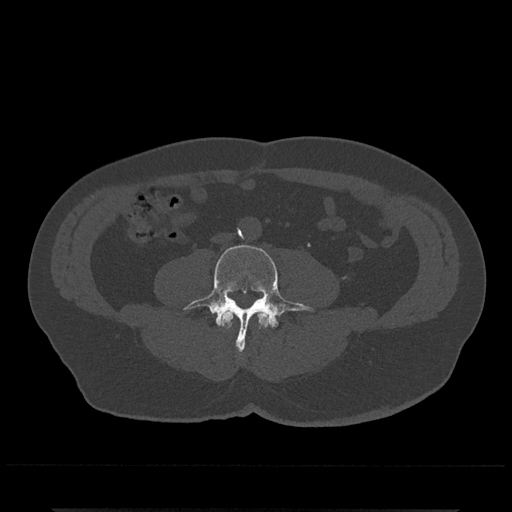
CT including the spine, one axial slice; slice 161 of 797 in the series (ordered by position); bone window (W 1800 / L 400 HU); 512 × 512 image matrix, field of view 393 × 393 mm. Male patient, age 67 years. From the clinical record (not read from this slice): primary cancer: prostate.
Outlined on this slice (semi-automatic segmentation, software-assisted and operator-edited):
- L3 vertebra: bounding box <220,310,270,328> (left, top, right, bottom; pixels)
- L4 vertebra: <183,244,315,351>